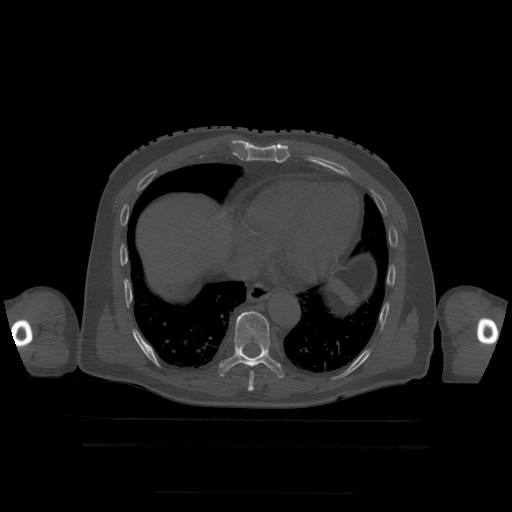
CT including the spine, one axial slice; position 263 of 522 along the scan axis; bone window (W 1800 / L 400 HU); 1.25 mm slice thickness; 512 × 512 image matrix, field of view 436 × 436 mm. Patient age 68 years. Case-level facts recorded for this patient, not image findings: primary cancer: urothelial.
Structures marked on this image (semi-automatically segmented with operator editing):
- T7 vertebra: box from (x=248, y=383) to (x=254, y=393) px
- T8 vertebra: (x=250, y=372)–(x=254, y=385)
- T9 vertebra: (x=218, y=311)–(x=284, y=379)